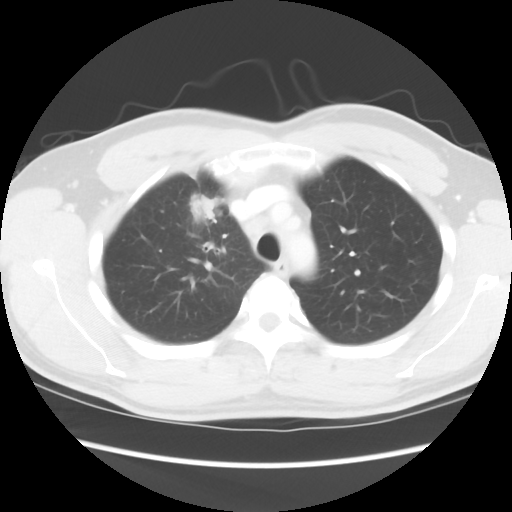
Chest CT, one axial slice. Position 67 of 80 along the scan axis. Reconstruction kernel STANDARD. 120 kVp. Lung window (W 1500 / L -600 HU). 5 mm slice thickness. 512 × 512 image matrix, field of view 360 × 360 mm. Male patient, age 35 years. Case-level facts recorded for this patient, not image findings: clinical TNM (as recorded): T1c N1 M1b.
Structures marked on this image (rectangle marked by the reading radiologist):
- lung tumour (recorded histology: adenocarcinoma): bounding box (x1, y1, x2, y2) in pixels: (189, 196, 225, 221)